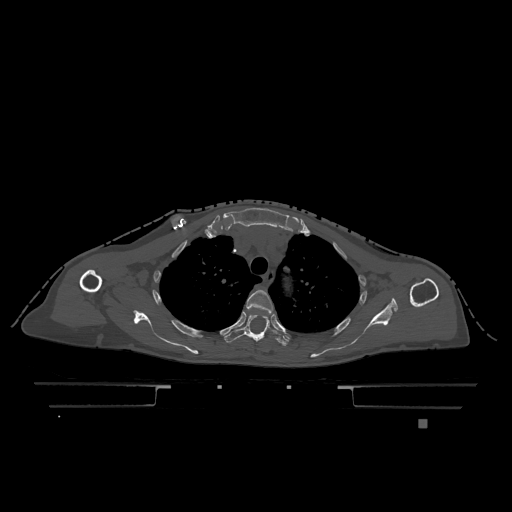
CT including the spine, one axial slice. Slice 897 of 1317 in the series (ordered by position). Bone window (W 1800 / L 400 HU). 0.5 mm slice thickness. 512 × 512 image matrix. Female patient, age 74 years. Case-level facts recorded for this patient, not image findings: primary cancer: lung; vertebrae with lytic lesions (as recorded): T1, T4, T5, T6, L4, L5.
Outlined on this slice (semi-automatically segmented with operator editing):
- T3 vertebra: bounding box <246,290,273,313> (left, top, right, bottom; pixels)
- T4 vertebra: <224,314,290,346>